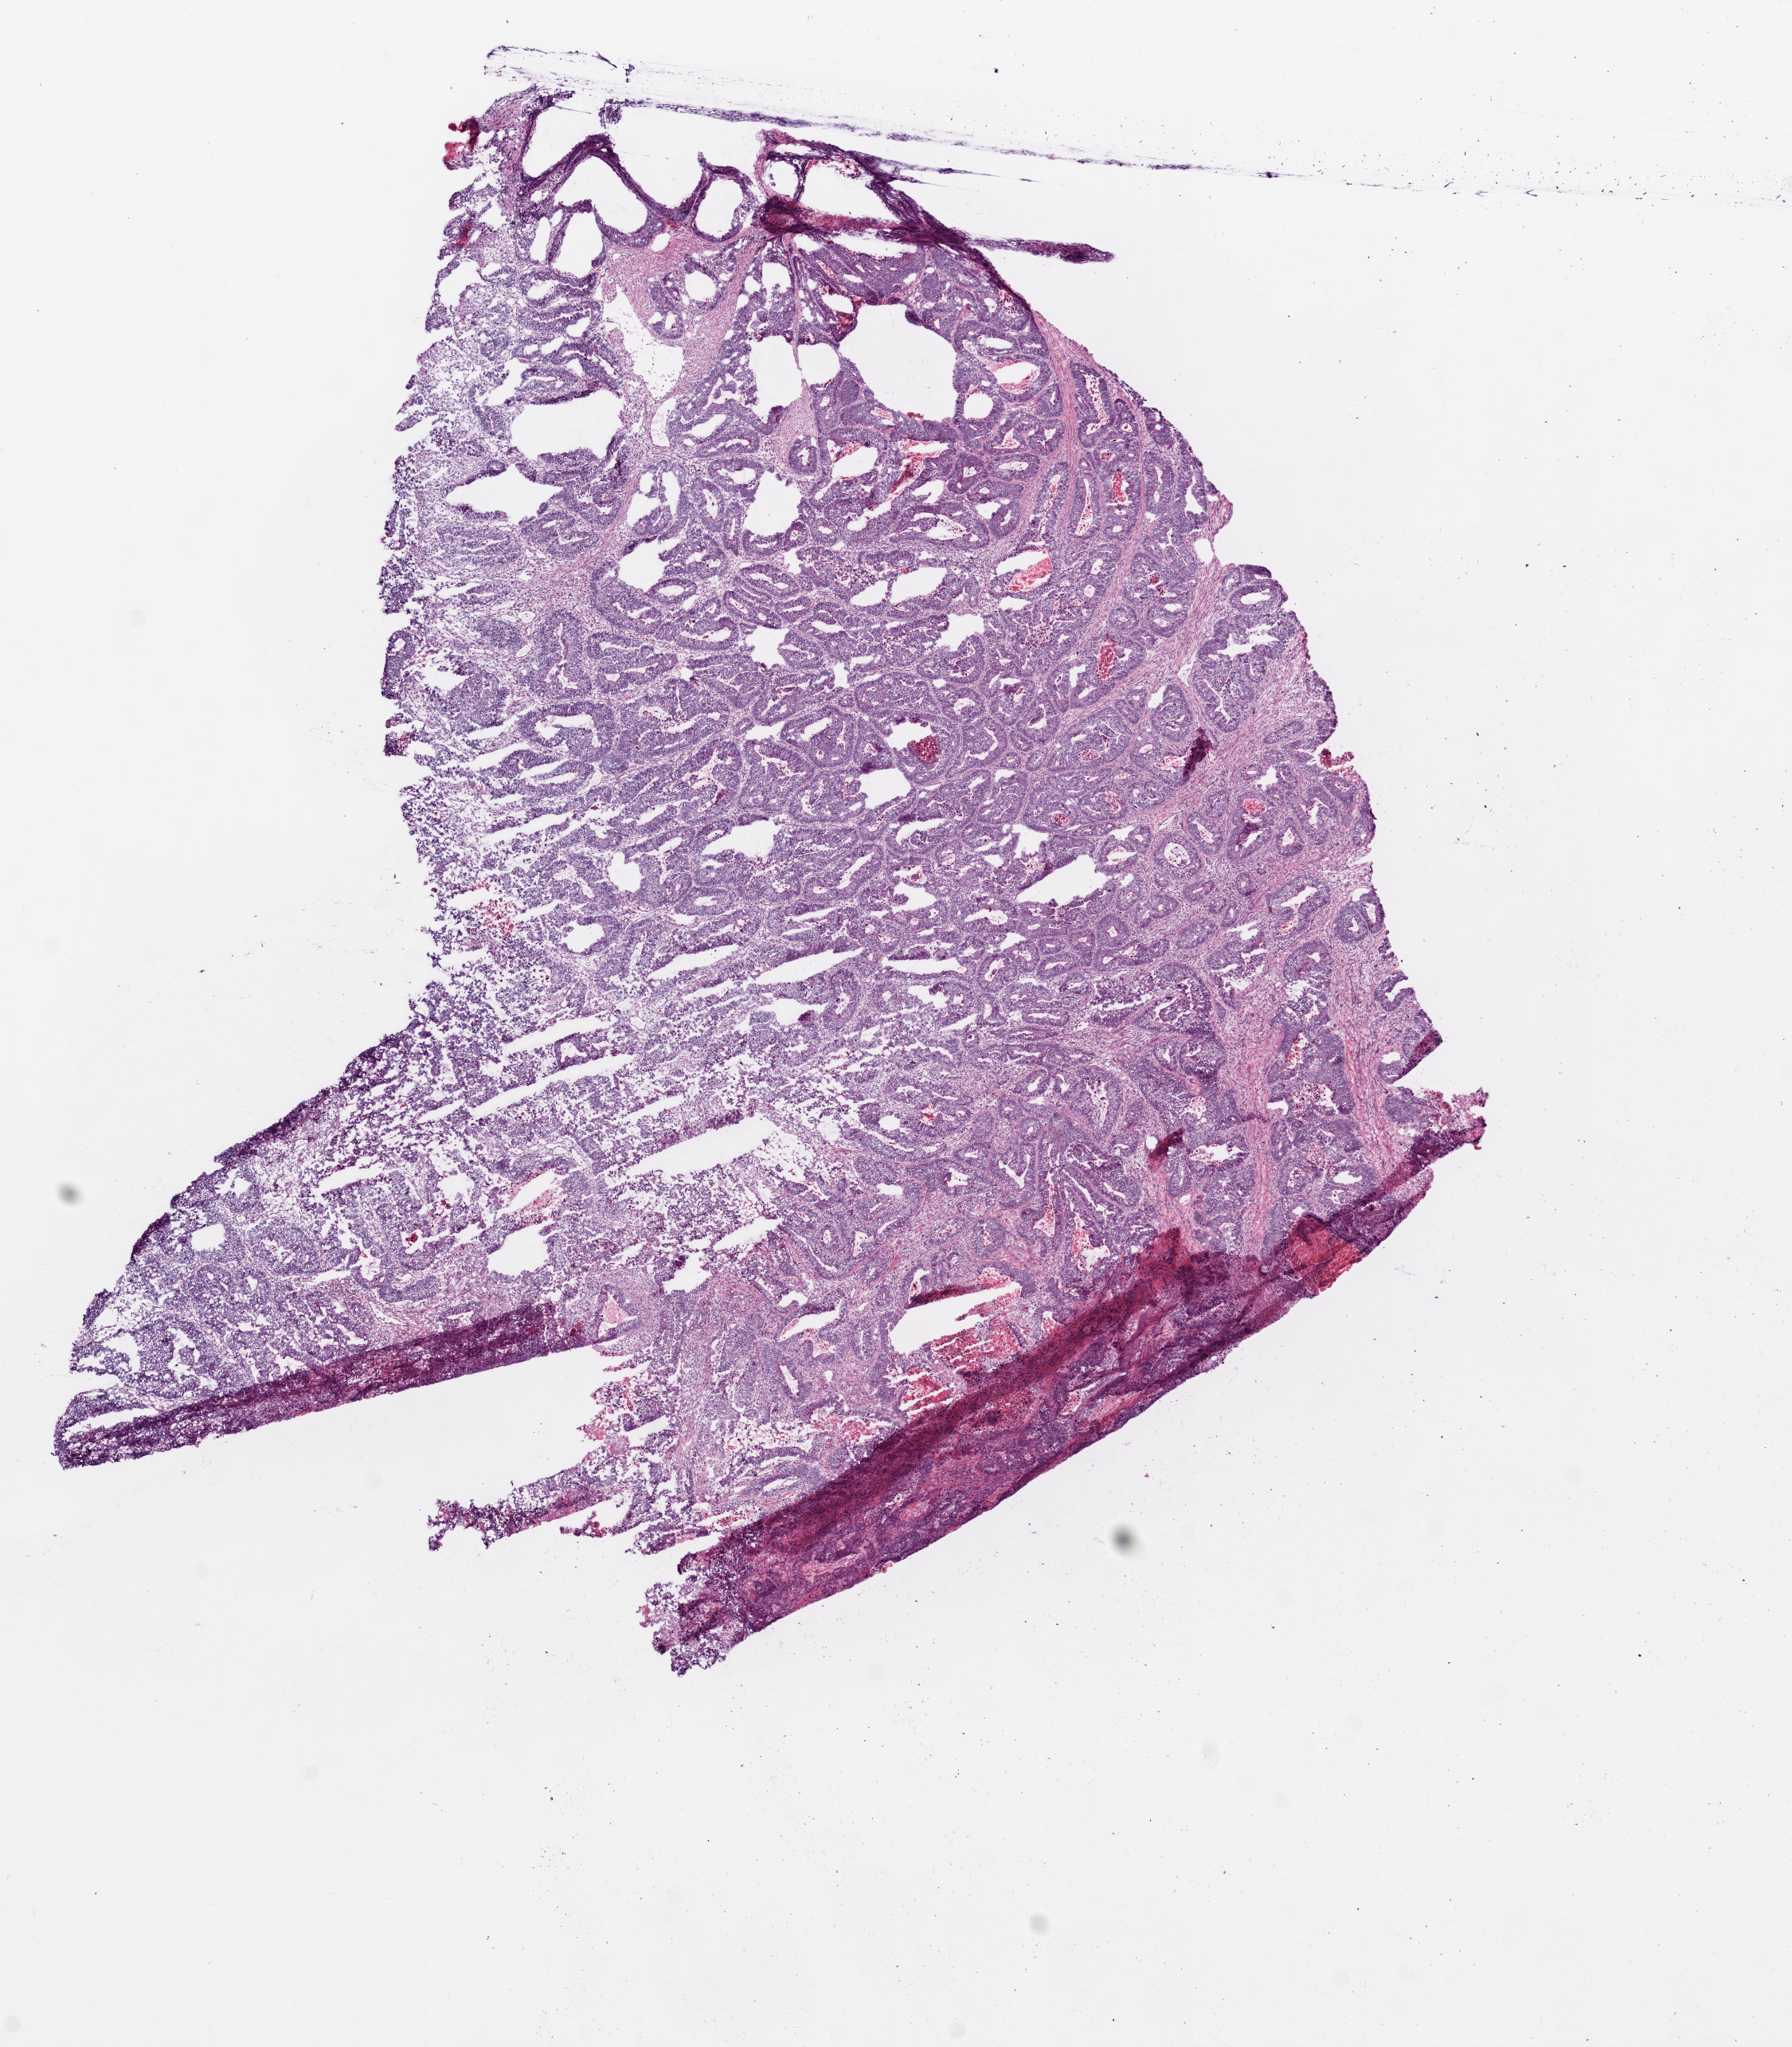
H&E-stained whole-slide image — whole scanned area (about 9.0 x 10.3 mm) shown as a low-resolution overview, frozen section, sample: primary tumour, rectum. Male, age 68 years at initial diagnosis. Pathologist review of this section (percent, as recorded): tumour cells 80%, tumour nuclei 85%, normal cells 10%, stromal cells 5%, necrosis 5%.
Lymph nodes positive (case pathology): 2 of 17 examined. Diagnosis: Adenocarcinoma, NOS (rectosigmoid junction). AJCC pathologic stage: IIIB (6th edition).